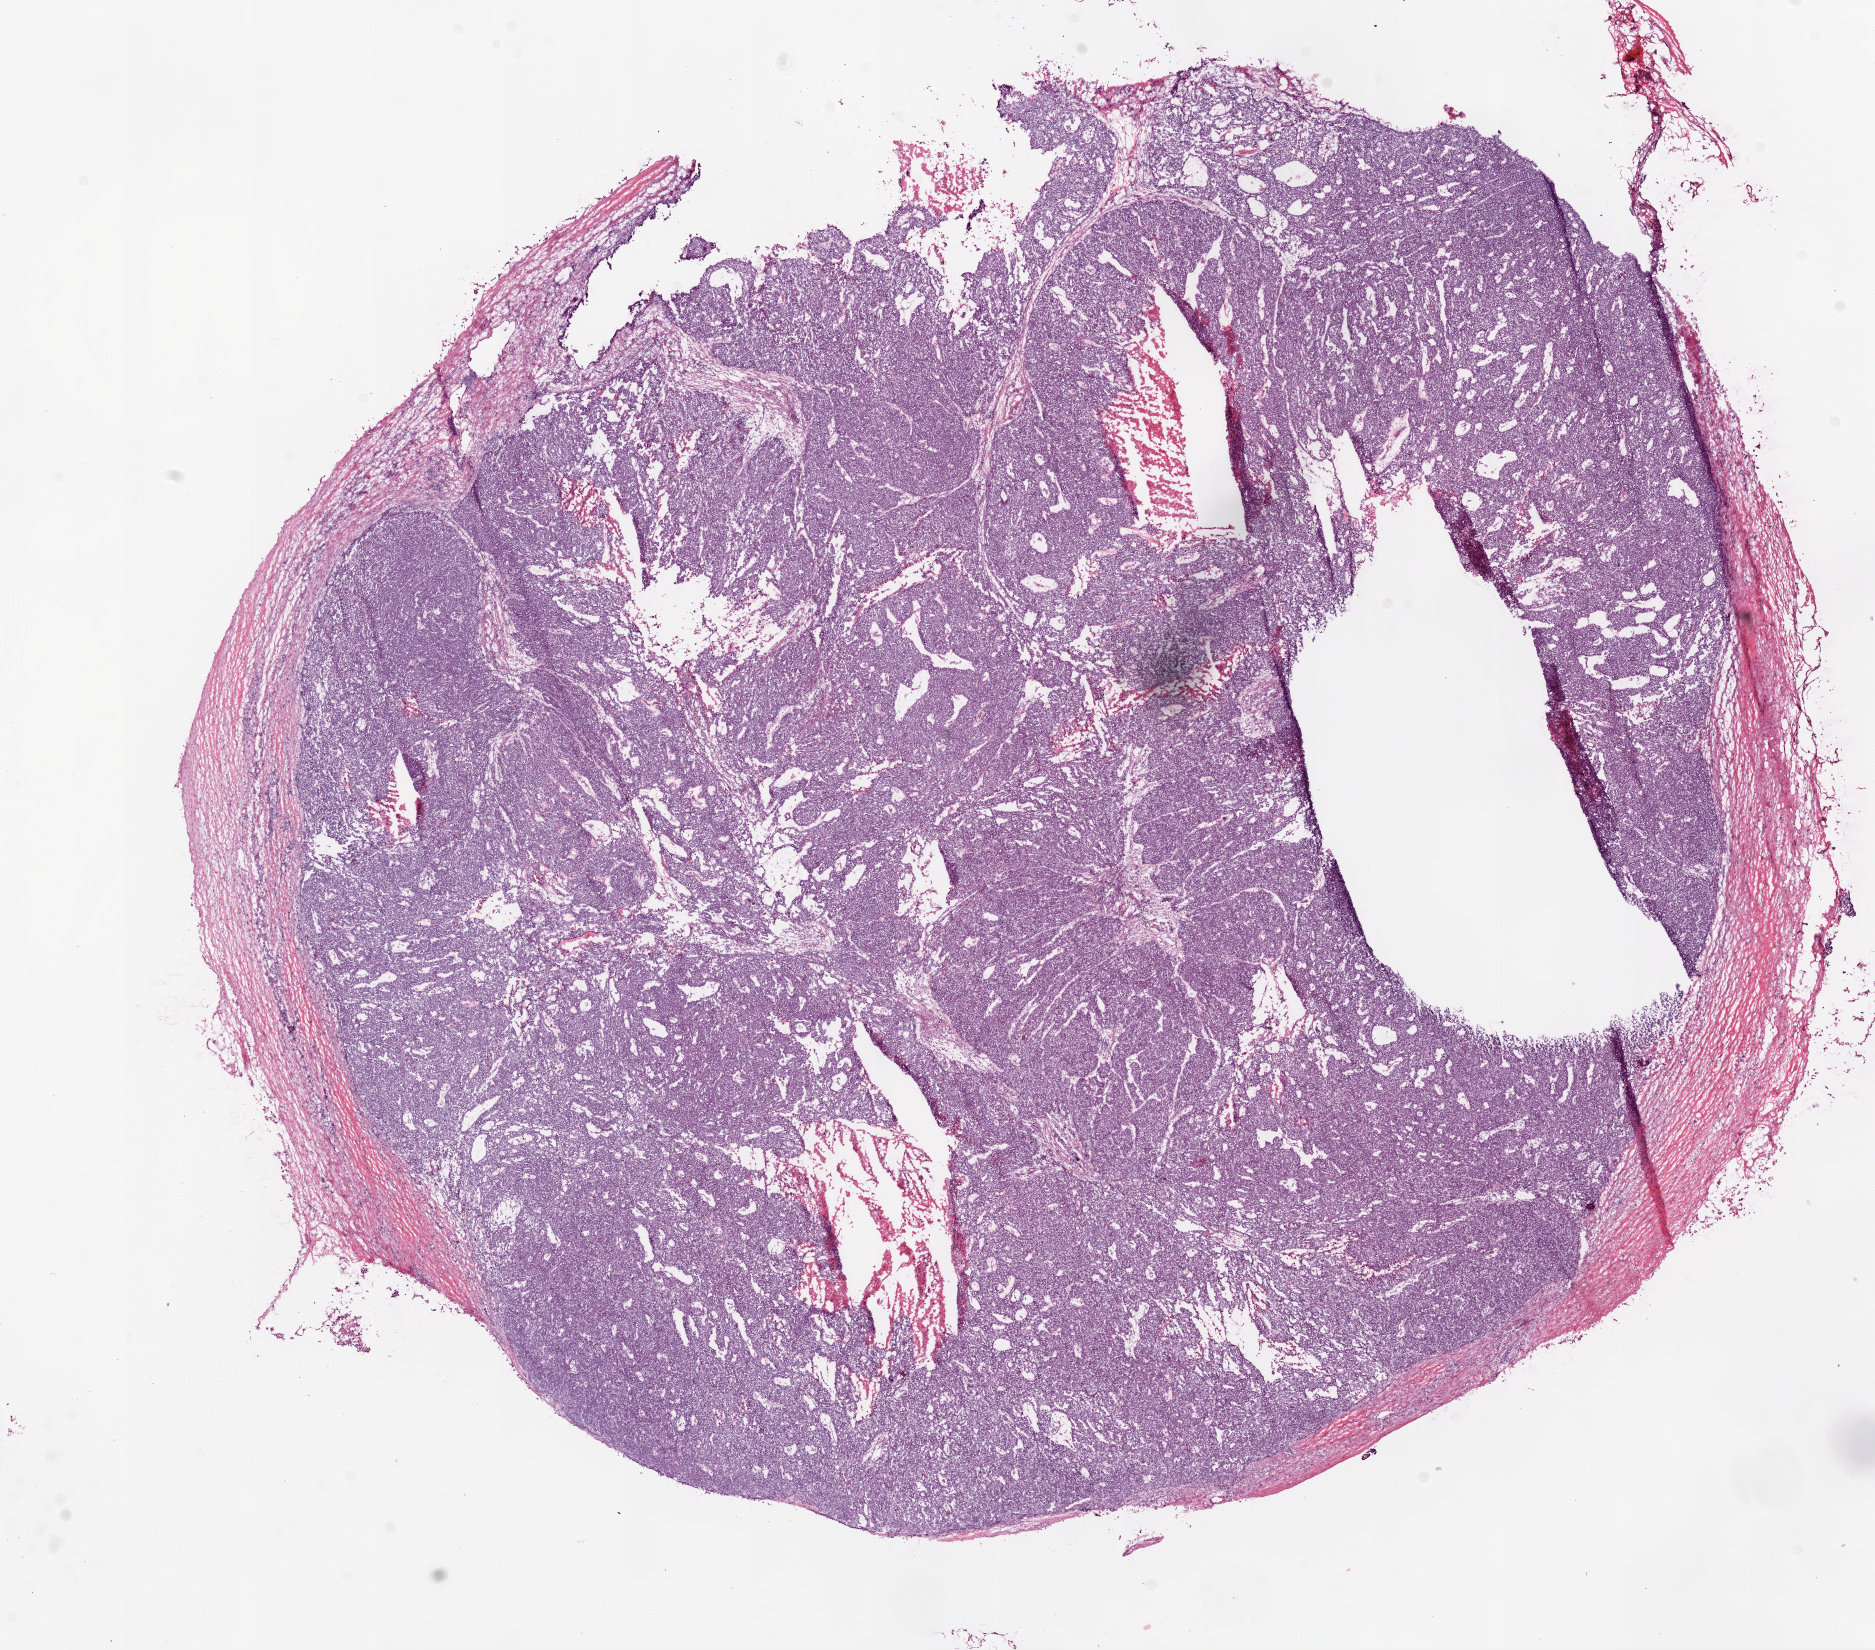
Digitized H&E-stained tissue section (whole slide) — a low-resolution overview of the entire scanned area, about 15.0 x 13.2 mm; frozen section; ovary, primary tumour sample. Patient: female, age at initial diagnosis 60 years. Histologic grade: G2 (moderately differentiated). Pathologist review of this section (percent, as recorded): tumour cells 80%, tumour nuclei 97%, normal cells 0%, stromal cells 10%, necrosis 10%.
Pathologic diagnosis: Serous cystadenocarcinoma, NOS. FIGO stage: IIIC.